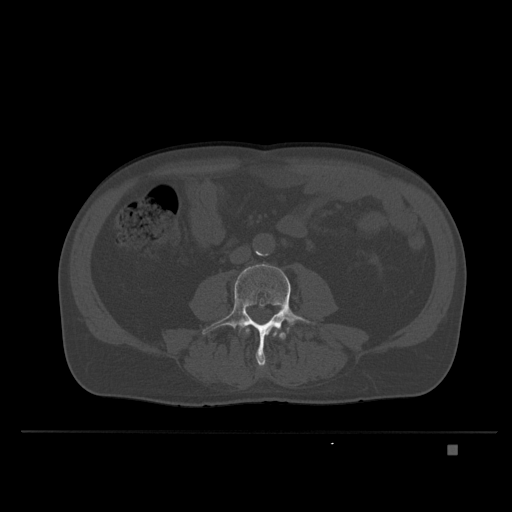
CT including the spine, one axial slice; position 78 of 435 along the scan axis; bone window (W 1800 / L 400 HU); 512 × 512 image matrix. Male patient, age 73 years. Case-level facts recorded for this patient, not image findings: primary cancer: skin.
Annotated regions visible in this slice (semi-automatic segmentation, software-assisted and operator-edited):
- L3 vertebra: box from (x=245, y=326) to (x=278, y=336) px
- L4 vertebra: (x=202, y=264)–(x=315, y=370)